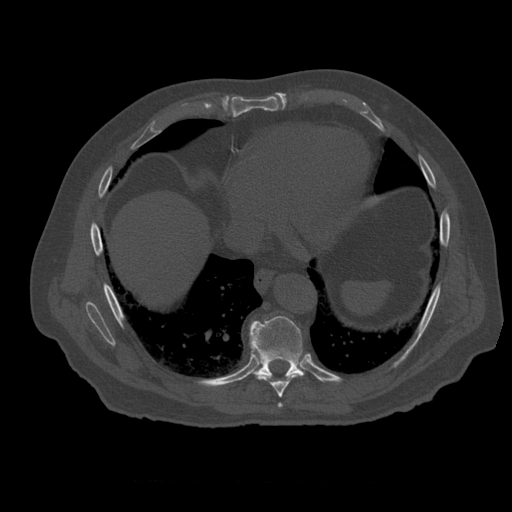
CT including the spine, one axial slice; position 330 of 399 along the scan axis; 120 kVp; bone window (W 1800 / L 400 HU); 1.25 mm slice thickness; 512 × 512 image matrix, field of view 407 × 407 mm. Patient age 73 years. Case-level facts recorded for this patient, not image findings: primary cancer: prostate; vertebrae with lytic lesions (as recorded): L2.
Structures marked on this image (semi-automatically segmented with operator editing):
- T7 vertebra: box from (x=279, y=404) to (x=283, y=407) px
- T8 vertebra: (x=258, y=375)–(x=302, y=398)
- T9 vertebra: (x=250, y=316)–(x=305, y=378)